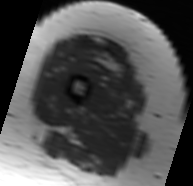
MRI of an extremity soft-tissue mass, one axial slice. Slice 17 of 91 in the series (ordered by position). MR volume resampled by the dataset authors to the PET/CT grid (not the native acquisition matrix). 3.27 mm slice thickness. 193 × 186 image matrix, field of view 188 × 182 mm. Female patient. From the clinical record (not read from this slice): histological type: malignant solitary fibrous tumor; grade: intermediate; site of the primary tumour: right thigh.
Annotated regions visible in this slice (expert contour drawn on MRI and transferred to this co-registered scan by the dataset authors):
- gross tumour volume including surrounding oedema: bounding box [x1, y1, x2, y2] px = [70, 37, 125, 77]